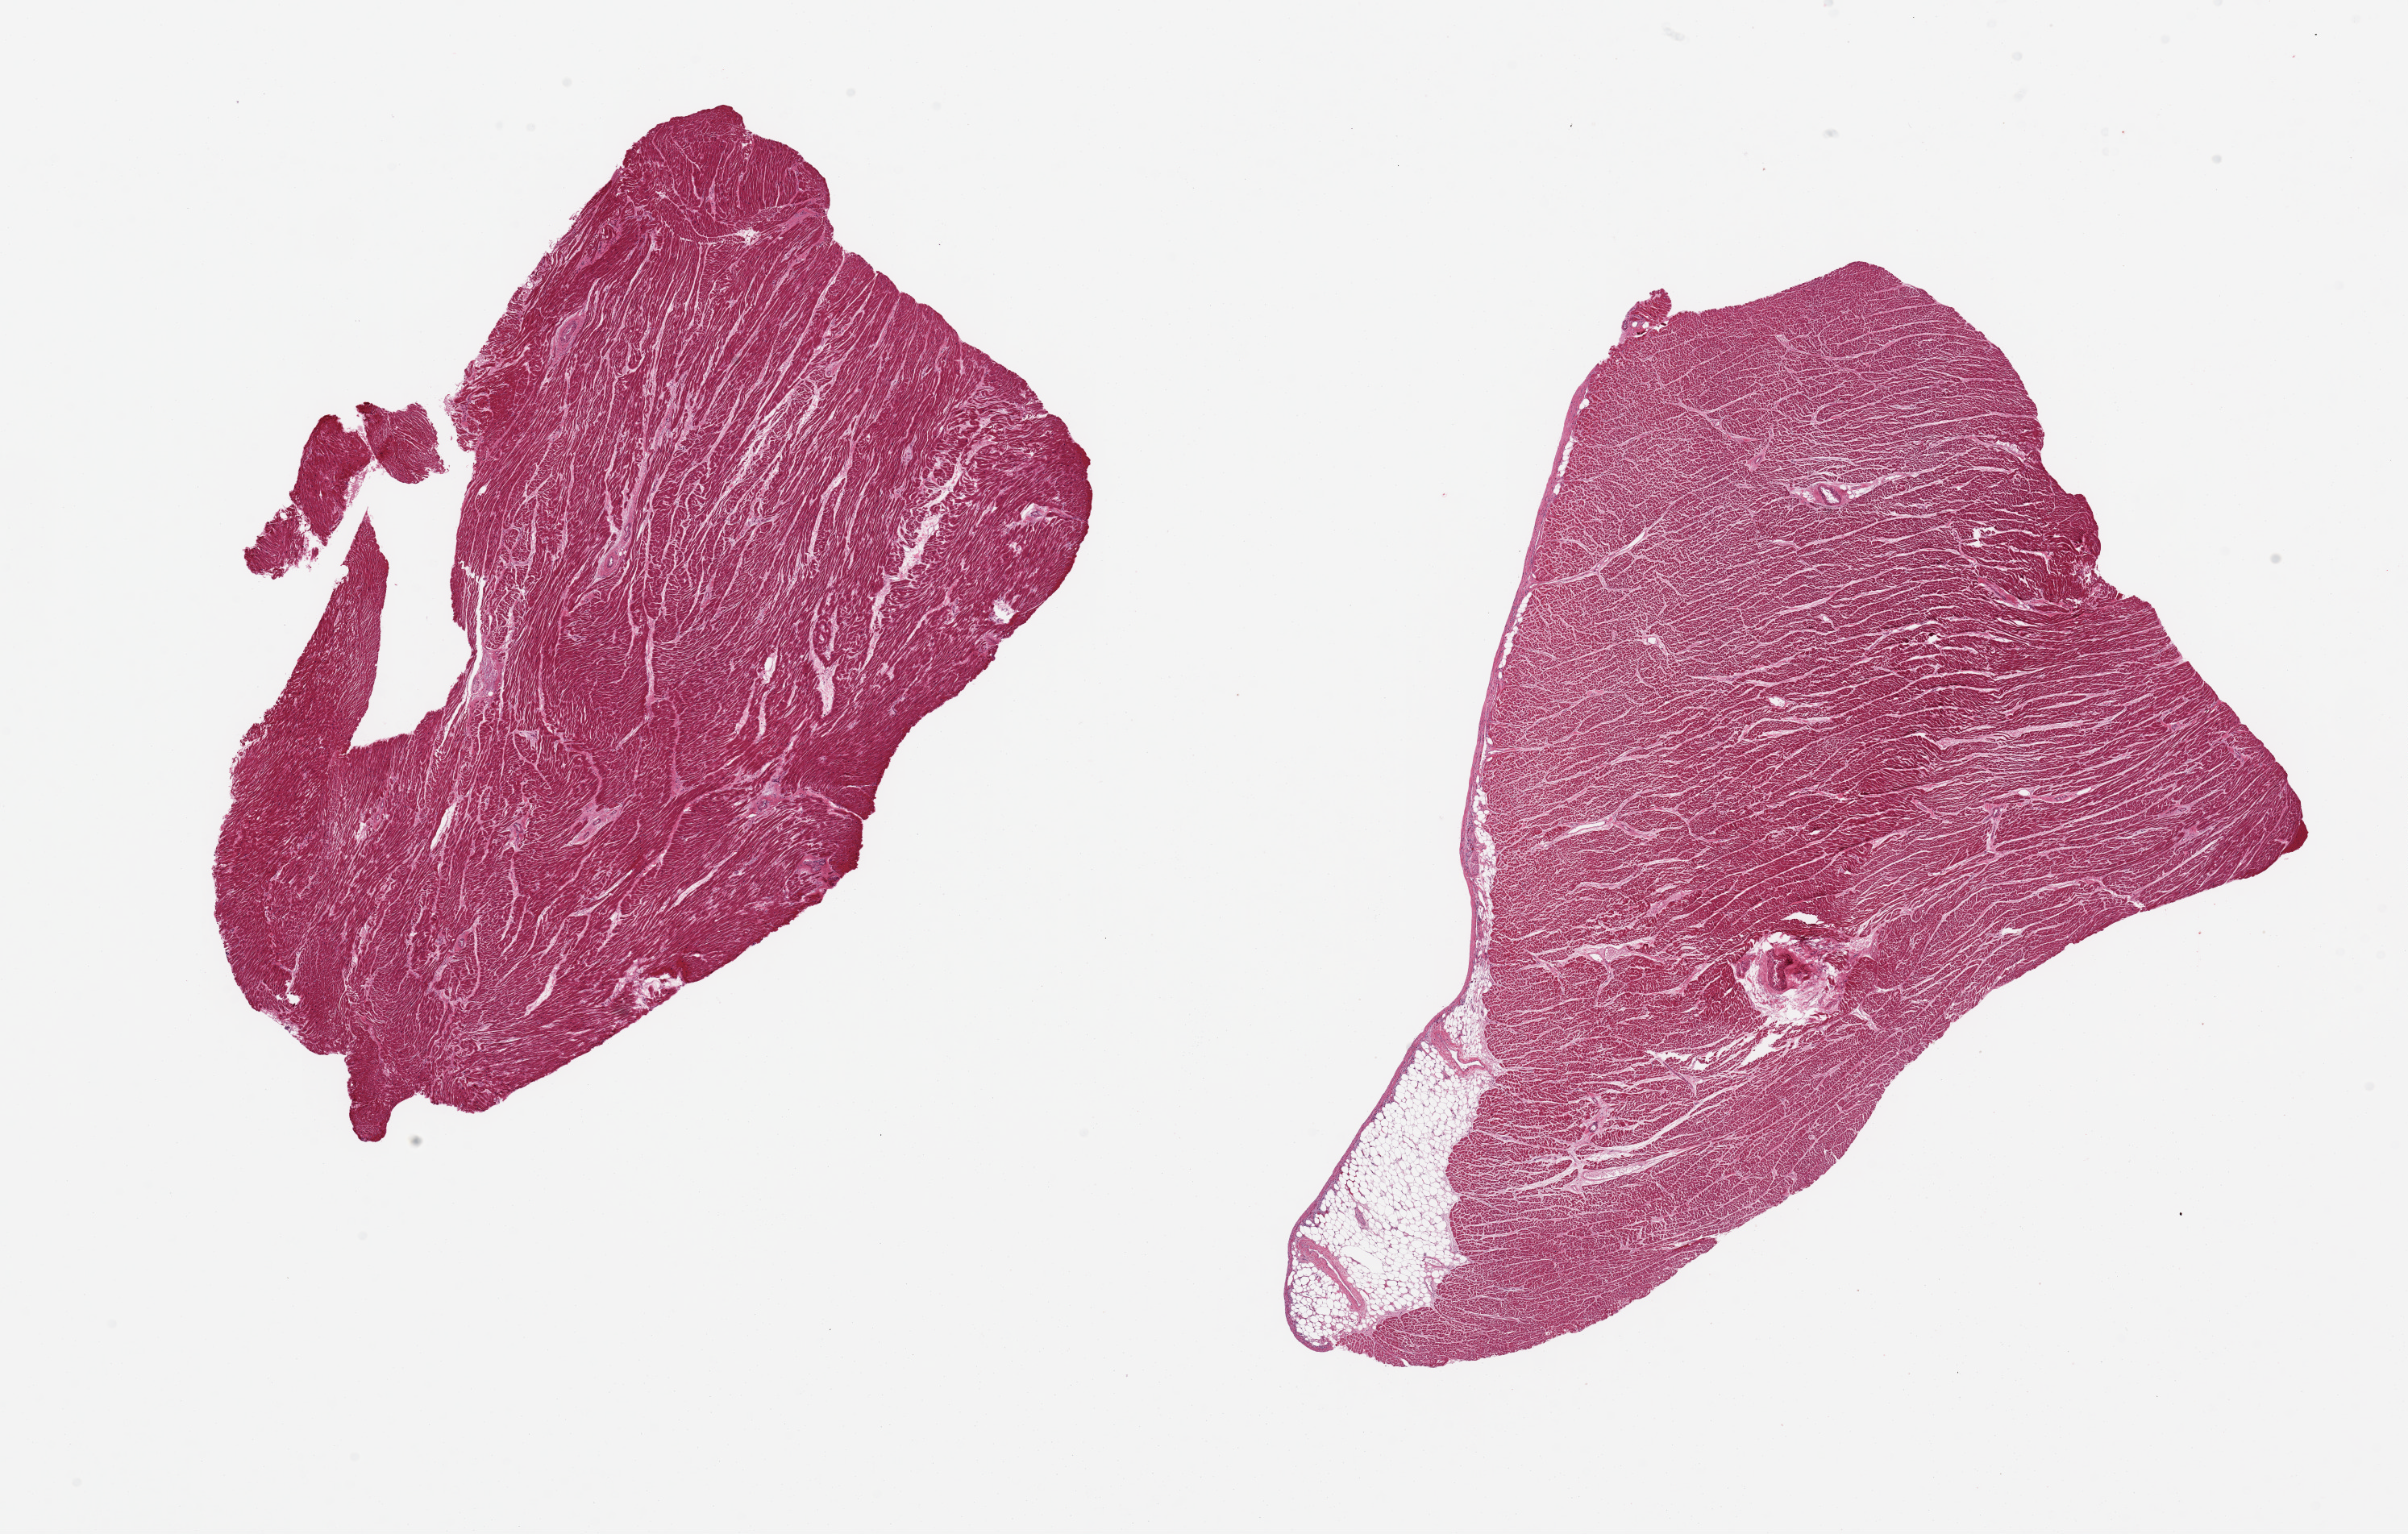
Hematoxylin and eosin (H&E) whole-slide image — a low-resolution overview of the entire scanned area, about 23.6 x 15.1 mm, PAXgene-fixed paraffin-embedded (PFPE) section, sampled site (target tissue): heart, donor tissue sample. Donor sex: male.
- reviewer comment on this tissue sample: 2 pieces, moderate interstitial fibrosis/chronic ischemic change